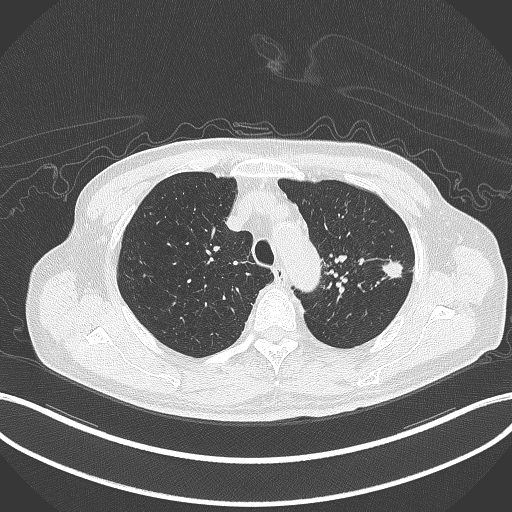
Chest CT, one axial slice; position 346 of 417 along the scan axis; 120 kVp; lung window (W 1500 / L -600 HU); 1 mm slice thickness; 512 × 512 image matrix, field of view 400 × 400 mm. Male patient, age 77 years. From the clinical record (not read from this slice): clinical TNM (as recorded): T3 N1 M0.
Structures marked on this image (bounding box drawn by a radiologist):
- lung tumour (recorded histology: adenocarcinoma): bounding box [x1, y1, x2, y2] px = [381, 256, 404, 280]